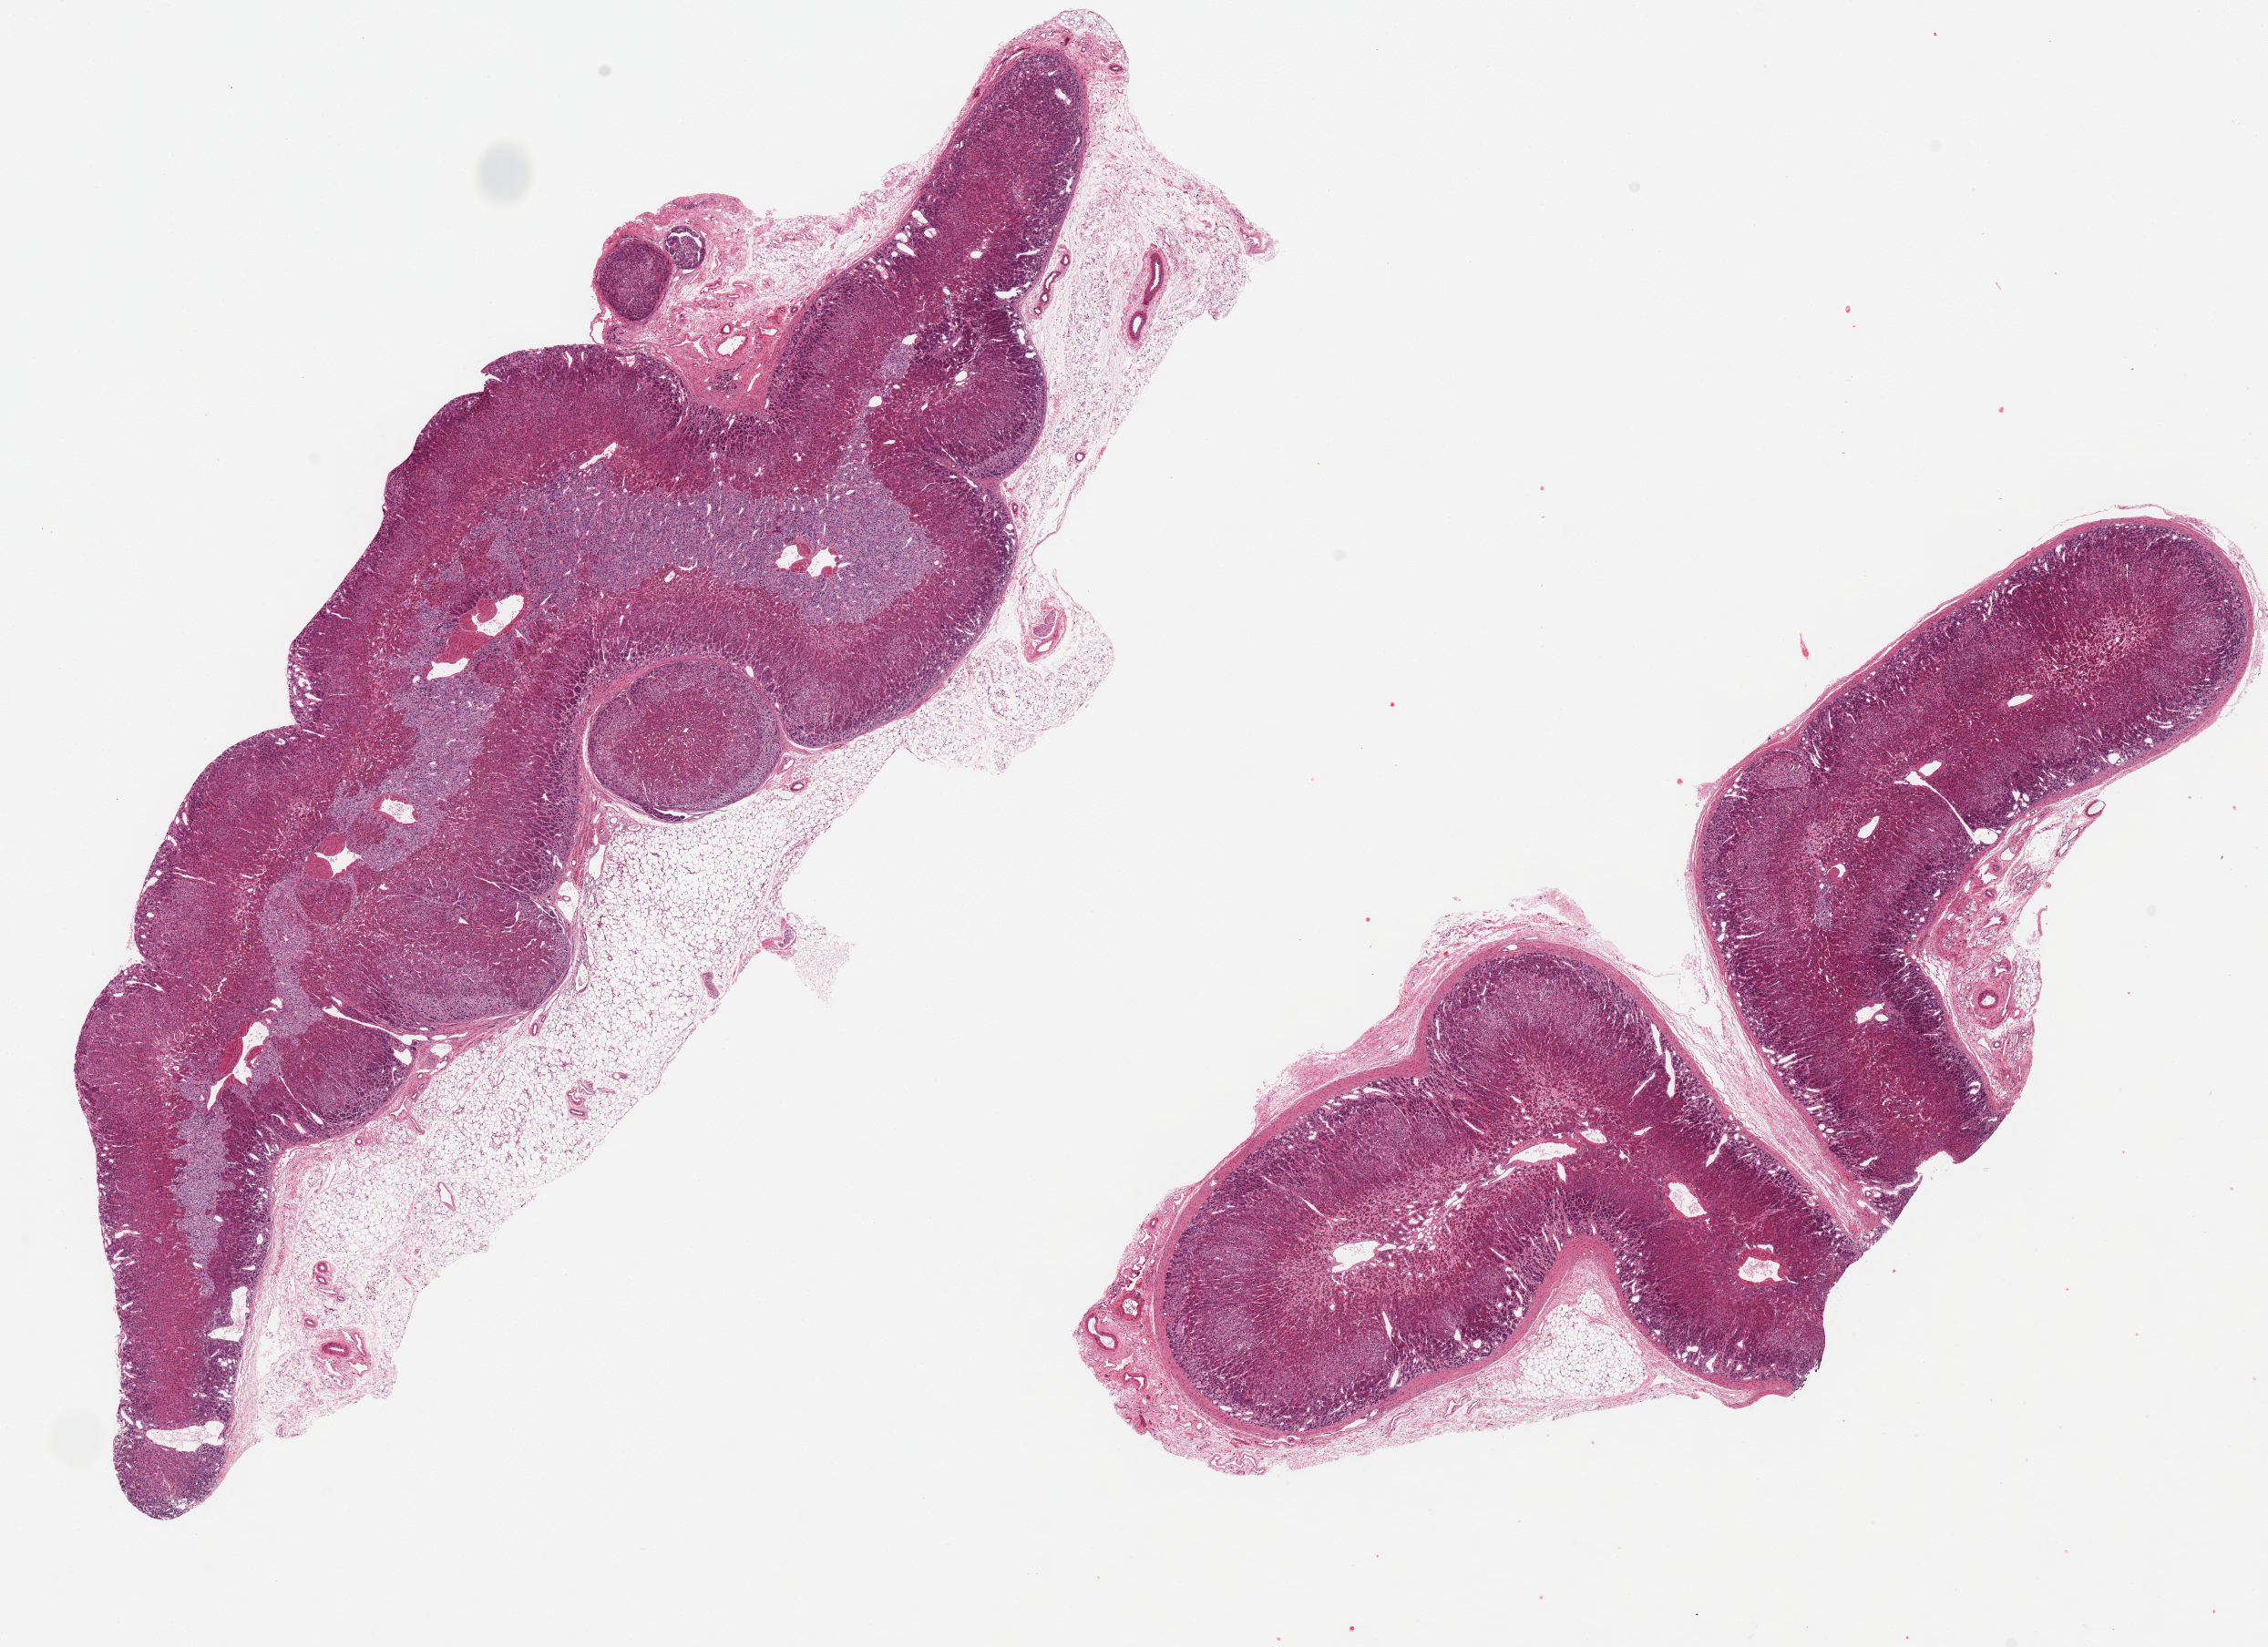
Digitized H&E-stained section, brightfield, whole scanned area (about 19.7 x 14.3 mm) shown as a low-resolution overview, PAXgene-fixed, paraffin-embedded tissue, sampled site (target tissue): adrenal gland, tissue donor sample. Female donor.
• review note (as recorded): 2 pieces, 15x5 mm; cortex & medulla well preserved; 30% periadrenal fat